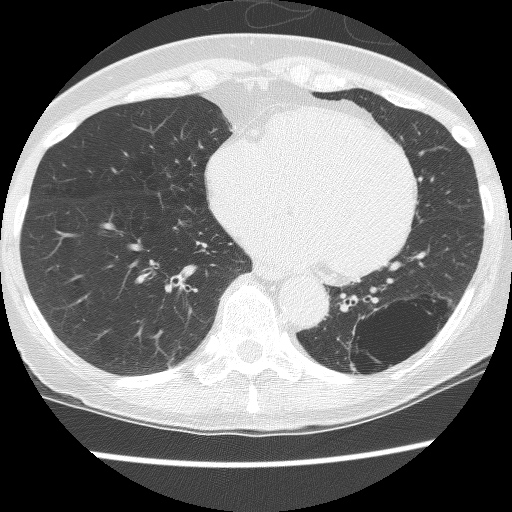
Axial slice from a low-dose chest CT screening exam; third screening round (two years after baseline); lung window (W 1500 / L -600 HU); 2.5 mm slice thickness; slice 86 of 130 in the series. Female, age 61 years at enrolment. Current smoker at enrolment.
• Expert reader's lesion annotation, bounding box (x1, y1, x2, y2) in pixels: (331, 291, 448, 390).
• The screening reader recorded 2 non-calcified nodules or masses ≥4 mm on this exam (left lower lobe, left lower lobe); which of them this box marks is not recorded.
• Official screen result: positive, no significant change: stable abnormalities potentially related to lung cancer, unchanged since the prior screening exam.
• Participant outcome: lung cancer diagnosed 166 days after this screen — non-small cell carcinoma, left lower lobe, poorly differentiated (G3), stage IB (AJCC 6th edition), 100 mm at pathology.